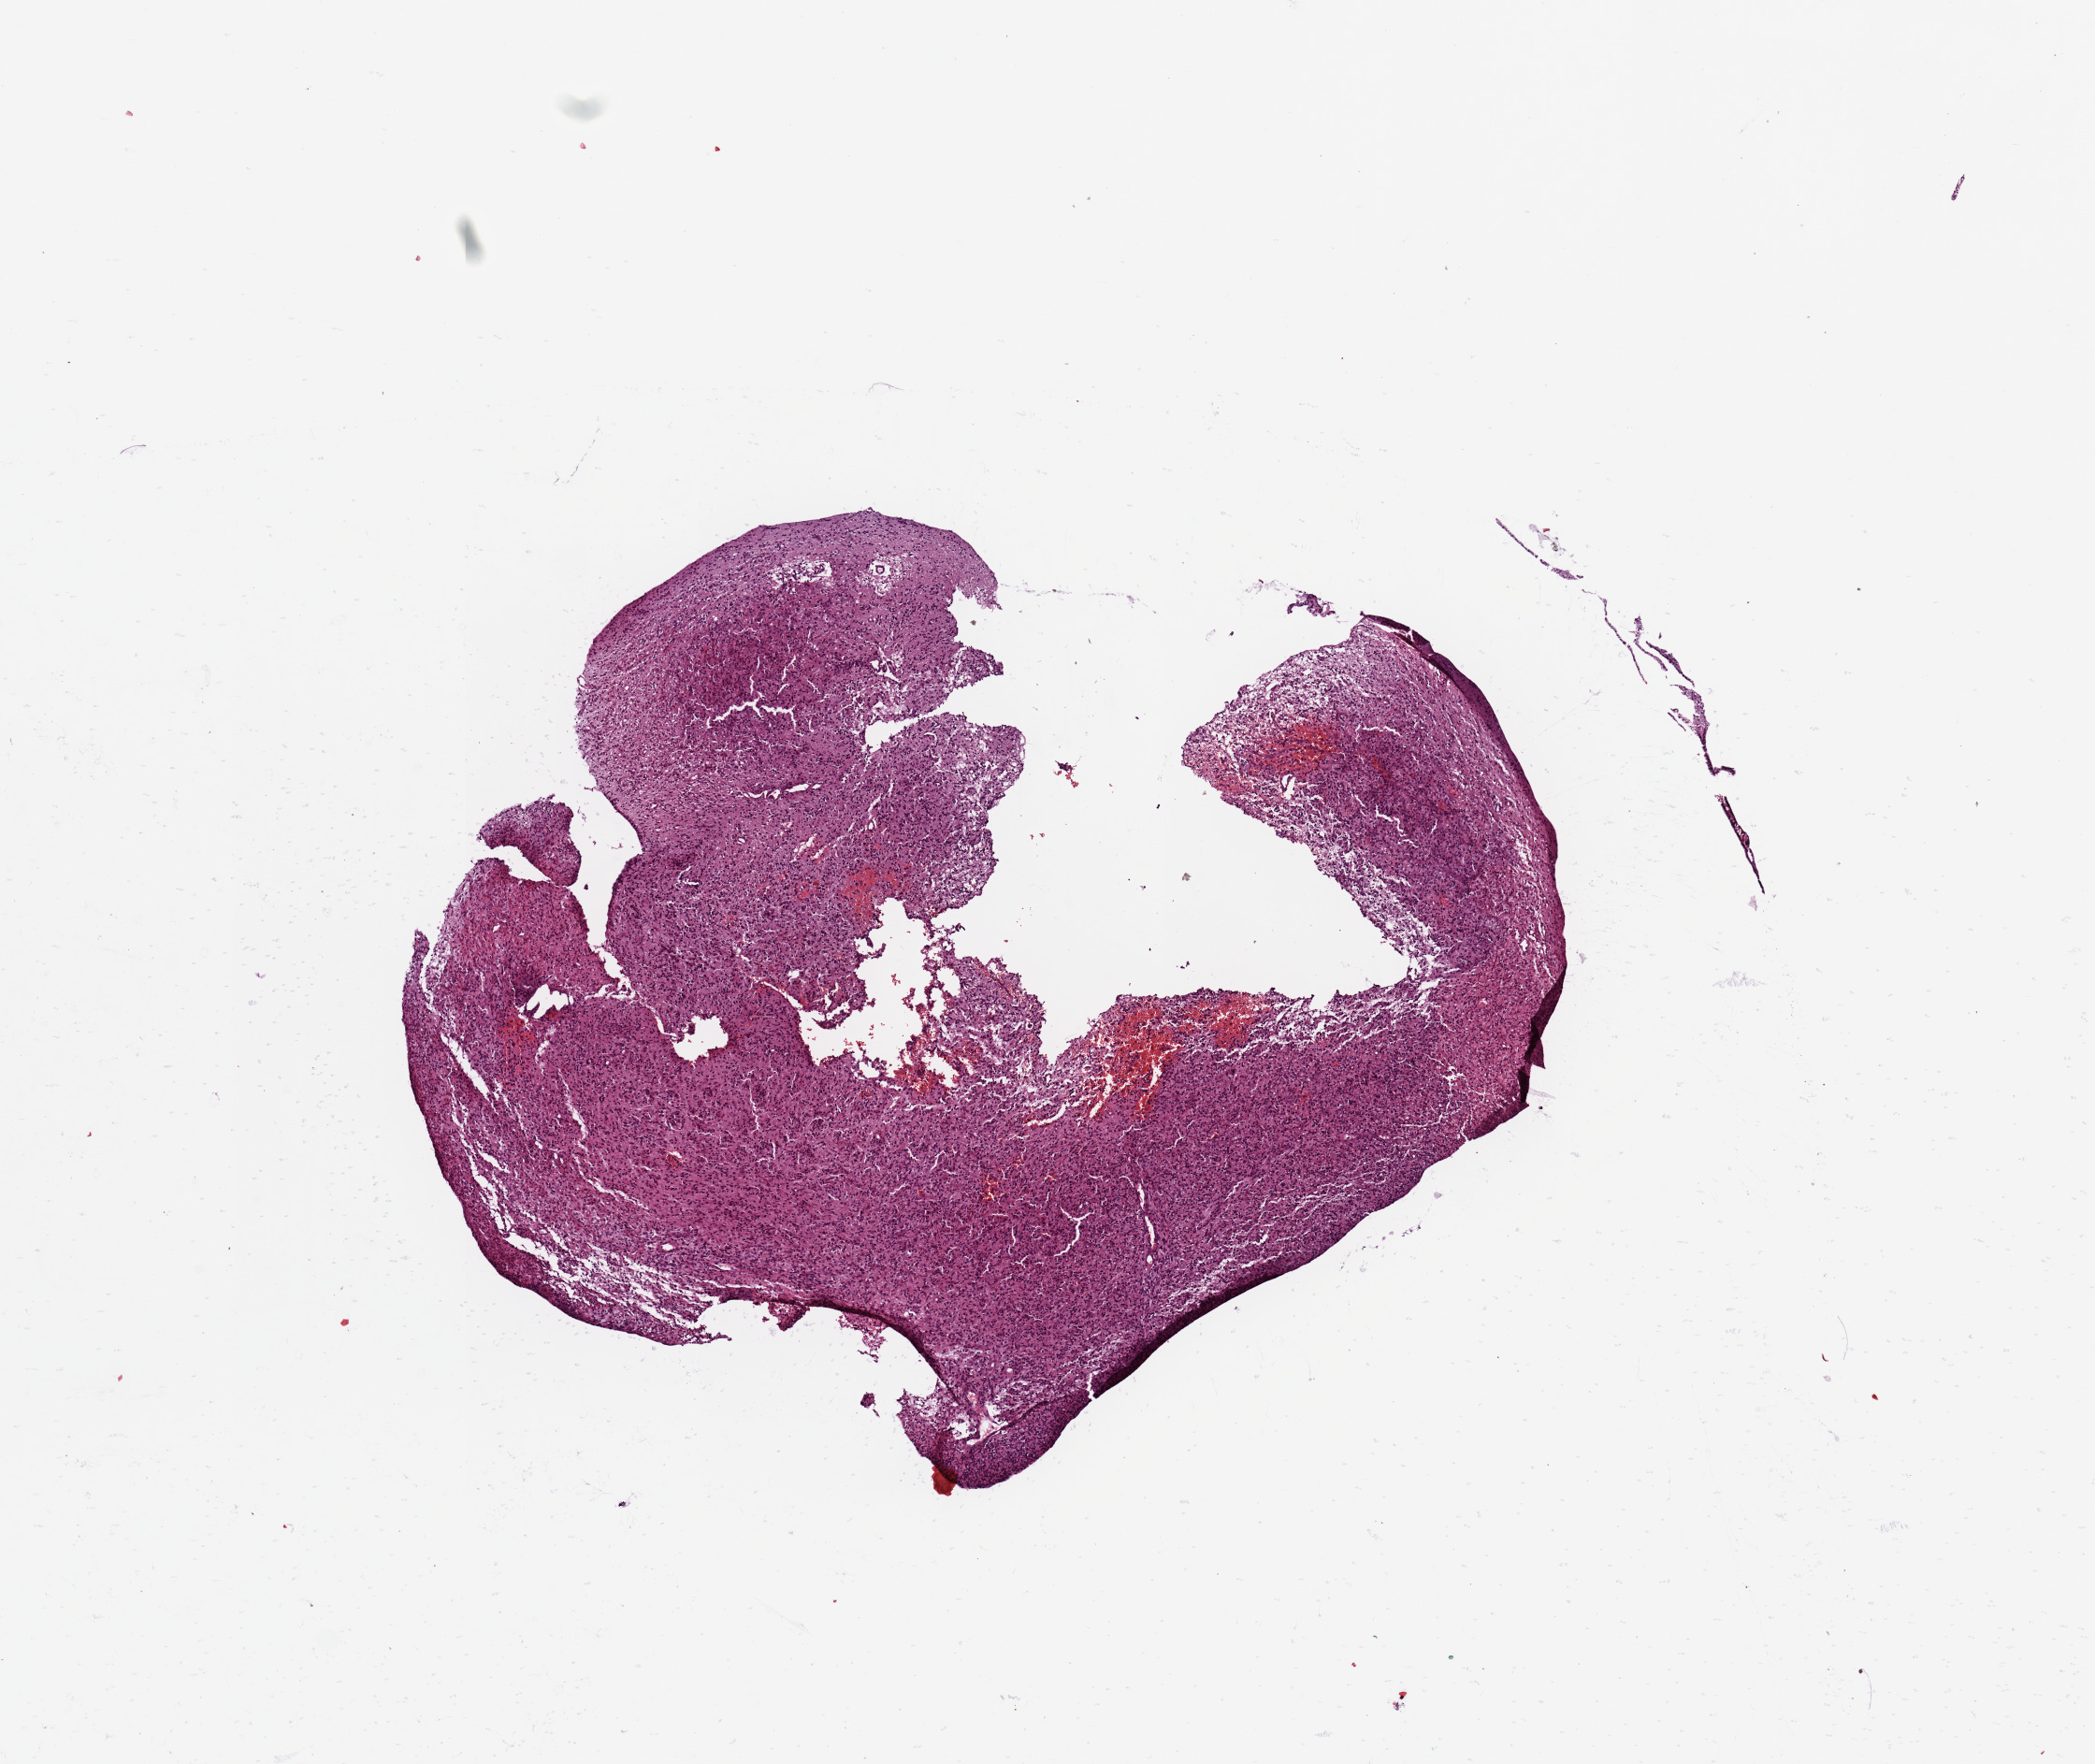
Digitized H&E tissue section (whole slide), shown as a low-resolution overview of the whole scanned area (about 8.9 x 7.5 mm, acquisition: 20x scan). Brain, tumour tissue. Male, 54 y/o.
- histologic diagnosis: Glioblastoma